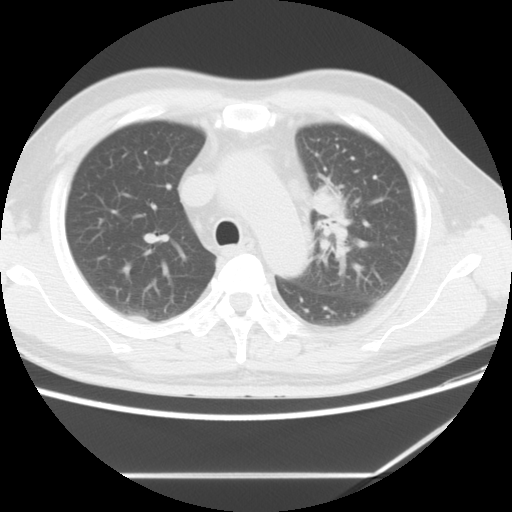
Chest CT, one axial slice. Position 4 of 10 along the scan axis. Reconstruction kernel STANDARD. Lung window (W 1500 / L -600 HU). 512 × 512 image matrix, field of view 350 × 350 mm. Patient: male, 56 years. Case-level facts recorded for this patient, not image findings: clinical TNM (as recorded): T2 N3 M1.
Structures marked on this image (rectangle marked by the reading radiologist):
- lung tumour (recorded histology: adenocarcinoma): bounding box (x1, y1, x2, y2) in pixels: (310, 189, 357, 263)